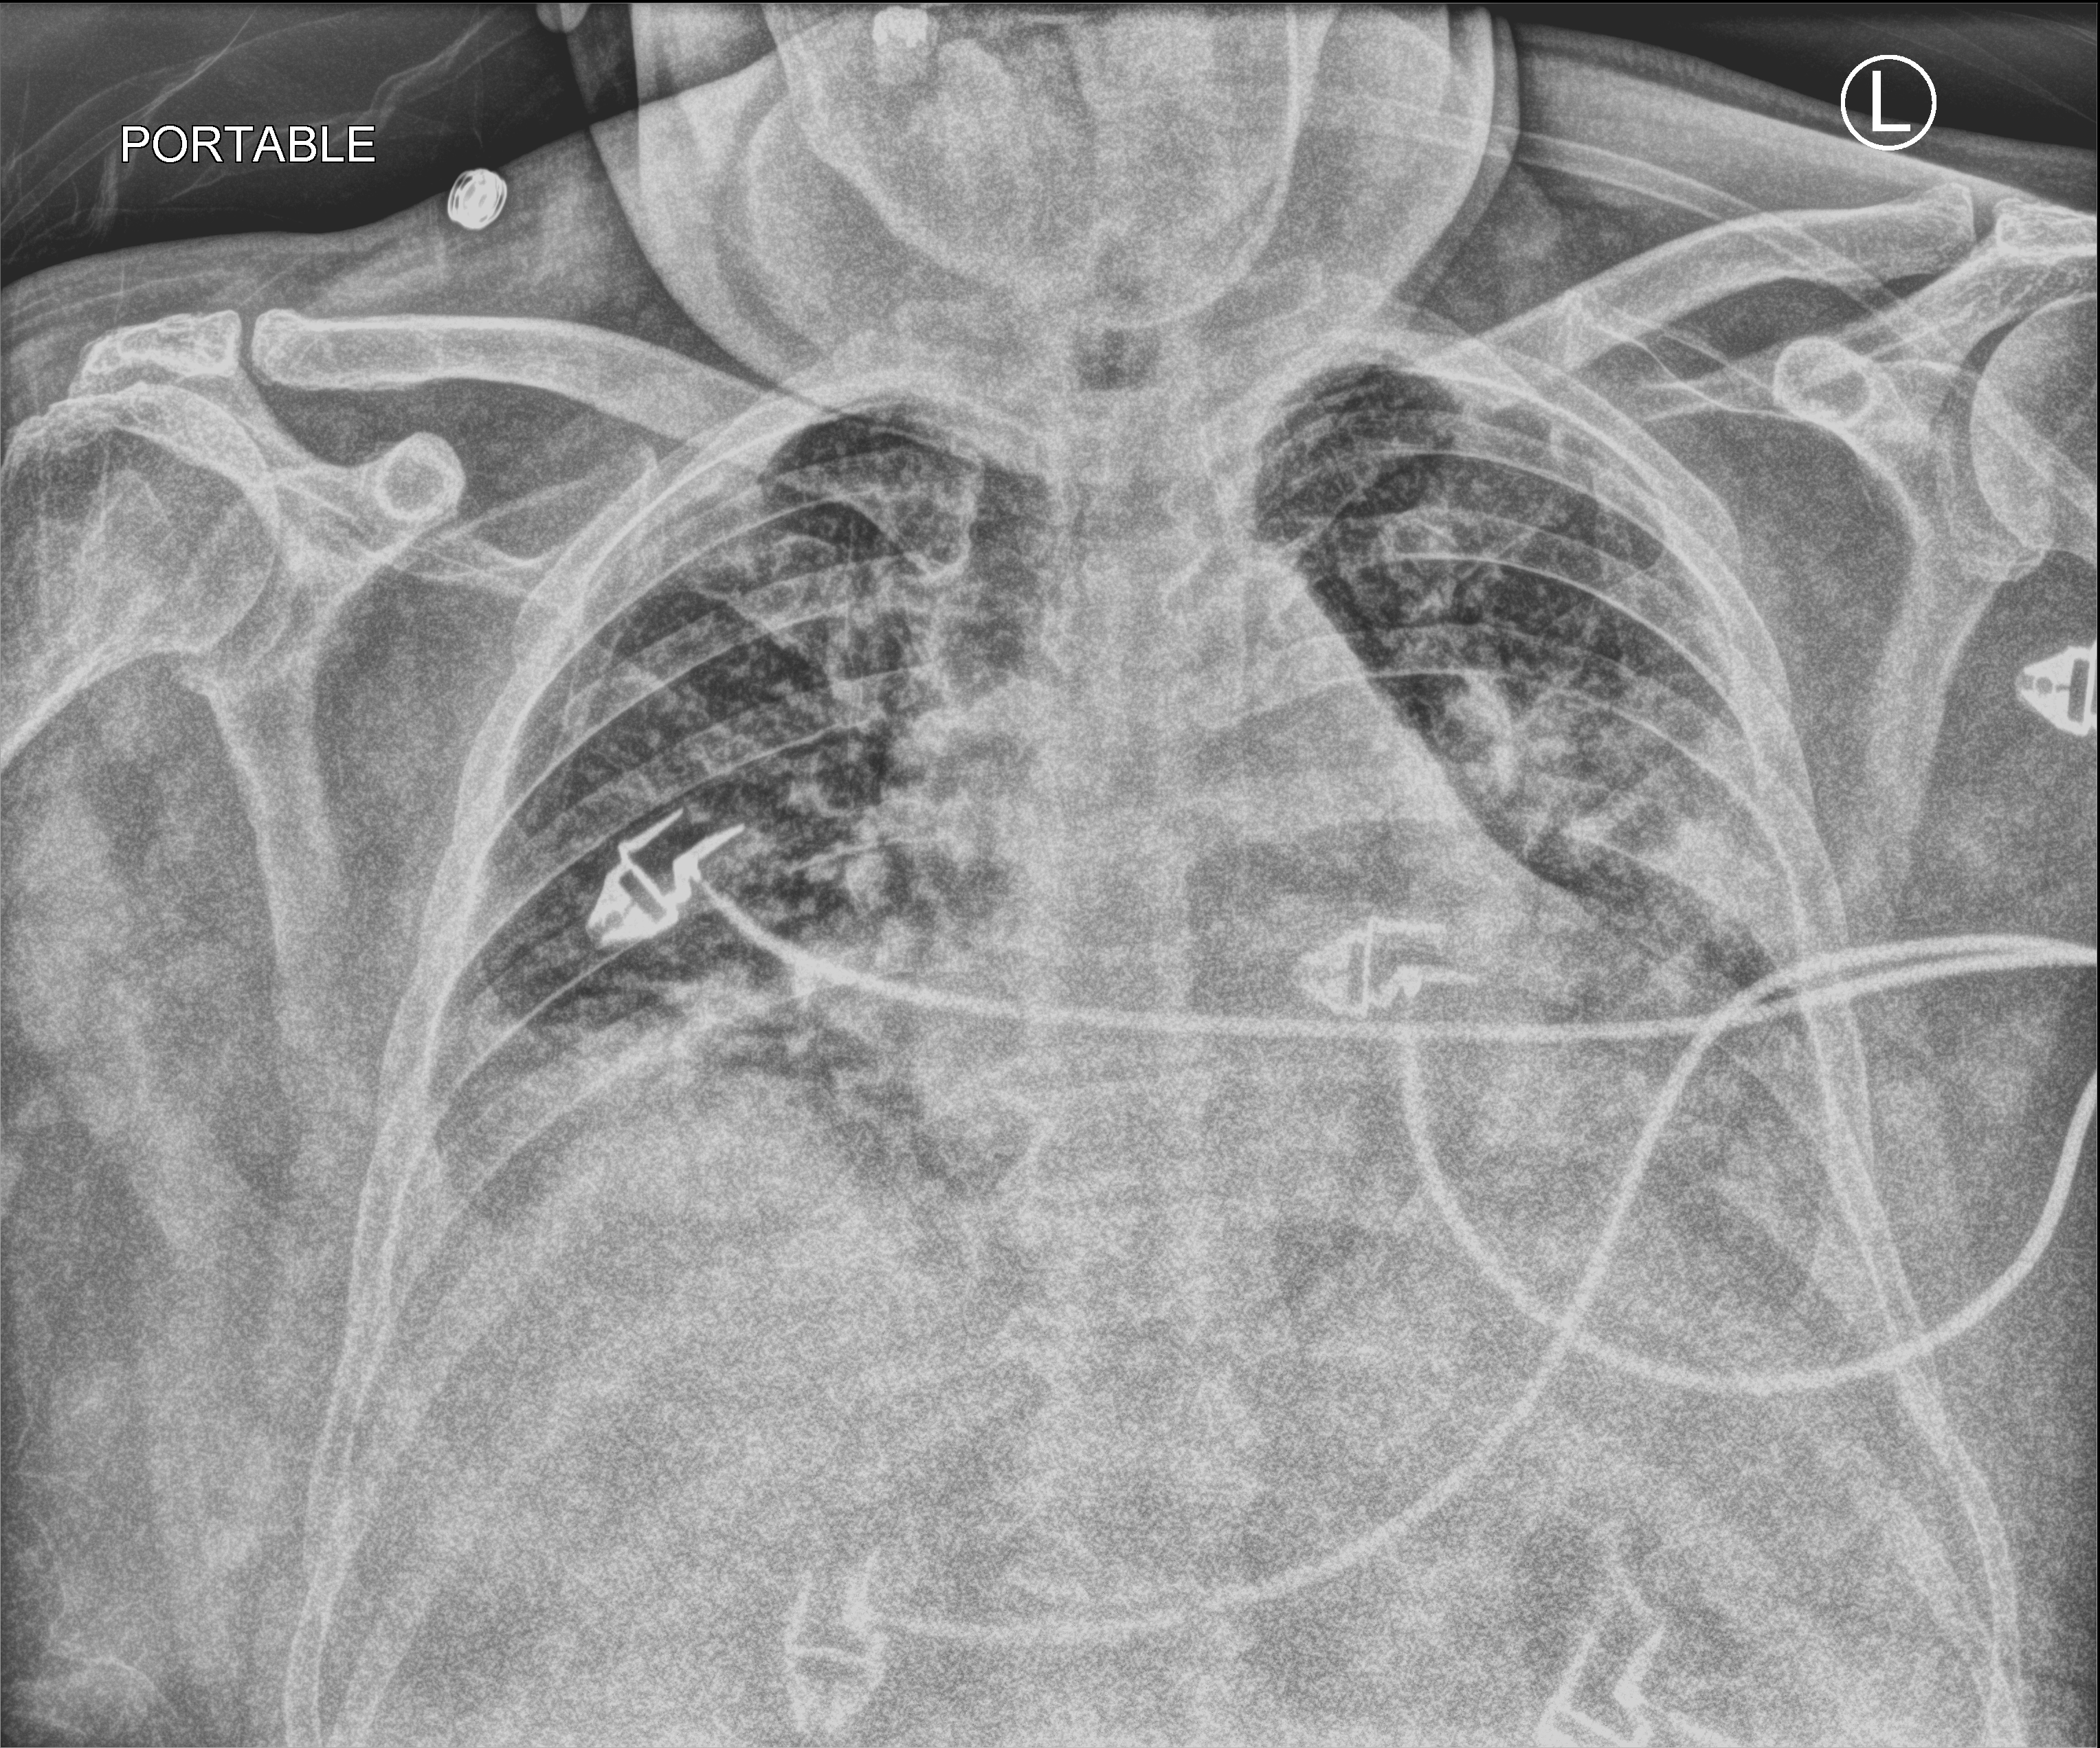
Bedside chest radiograph (computed radiography); anteroposterior (AP) projection. Male patient hospitalised with COVID-19, age 60–74 years.
From the hospital-stay record, not from the radiograph (when in the stay this image was taken is not recorded):
- mechanically ventilated during this hospital stay: yes
- length of hospital stay: 26 days